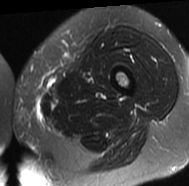
MRI of an extremity soft-tissue mass, one axial slice; position 14 of 77 along the scan axis; T2-weighted fat-saturated; MR volume resampled by the dataset authors to the PET/CT grid (not the native acquisition matrix); 3.27 mm slice thickness; 189 × 186 image matrix, field of view 185 × 182 mm. Female patient. From the clinical record (not read from this slice): histological type: leiomyosarcoma; grade: high; site of the primary tumour: groin.
Structures marked on this image (expert contour drawn on MRI and transferred to this co-registered scan by the dataset authors):
- gross tumour volume including surrounding oedema: bounding box [x1, y1, x2, y2] px = [15, 111, 43, 123]